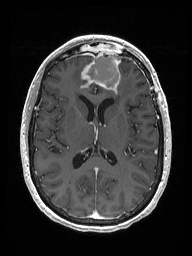
Brain MRI from a brain-tumour surgery series, one axial slice; T1-weighted post-contrast; 1 mm slice thickness; 192 × 256 image matrix, field of view 187 × 250 mm. Case-level facts recorded for this patient, not image findings: histopathology: Metastastic Carcinoma from Breast primary; tumour location: Right Frontal.
Structures marked on this image (outlined manually by an expert reader):
- previous resection cavity: bounding box (x1, y1, x2, y2) in pixels: (88, 52, 121, 88)